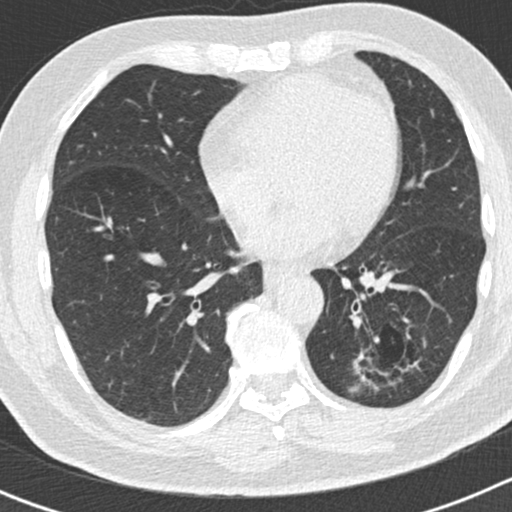
Chest CT (low-dose screening protocol), one axial image. Second screening round (one year after baseline). Lung window (W 1500 / L -600 HU). 2 mm slice thickness. Standard (soft-tissue) reconstruction kernel (B30f). Slice 100 of 186 in the series. Male participant, aged 66 years at enrolment. Former smoker at enrolment.
- Expert reader's lesion annotation, bounding box [x1, y1, x2, y2] px = [346, 324, 417, 403].
- Screening reader's record for this exam (one nodule recorded; not confirmed to be the boxed lesion): non-calcified nodule or mass ≥4 mm, left lower lobe, 50 × 33 mm, smooth margins, pre-existing on the prior screen: yes; interval growth: yes.
- Official screen result: positive, other.
- Lung cancer was diagnosed 440 days after this screen: adenocarcinoma, NOS, left lower lobe, poorly differentiated (G3), stage IB (AJCC 6th edition), 38 mm at pathology.